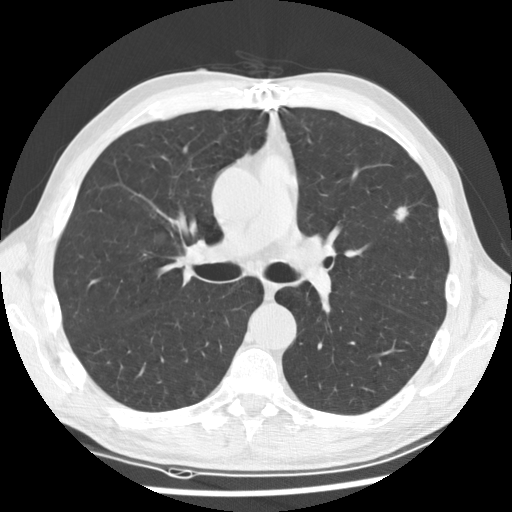
Low-dose screening chest CT, axial slice; baseline screening round; lung window (W 1500 / L -600 HU); 2.5 mm slice thickness; standard (soft-tissue) reconstruction kernel (STANDARD); 512 × 512 image matrix, field of view 340 × 340 mm. Male participant, aged 64 years at enrolment.
Expert reader's lesion annotation, bounding box <377,198,428,240> (left, top, right, bottom; pixels). The exam's reader record, not a measurement of the box and not confirmed to be the same lesion: non-calcified nodule or mass ≥4 mm, left upper lobe, 13 × 10 mm, spiculated (stellate) margins, soft tissue attenuation. Participant outcome: lung cancer diagnosed 410 days after this screen (after the second annual screen) — adenocarcinoma, NOS, left upper lobe, poorly differentiated (G3), stage IA (AJCC 6th edition), 10 mm at pathology.